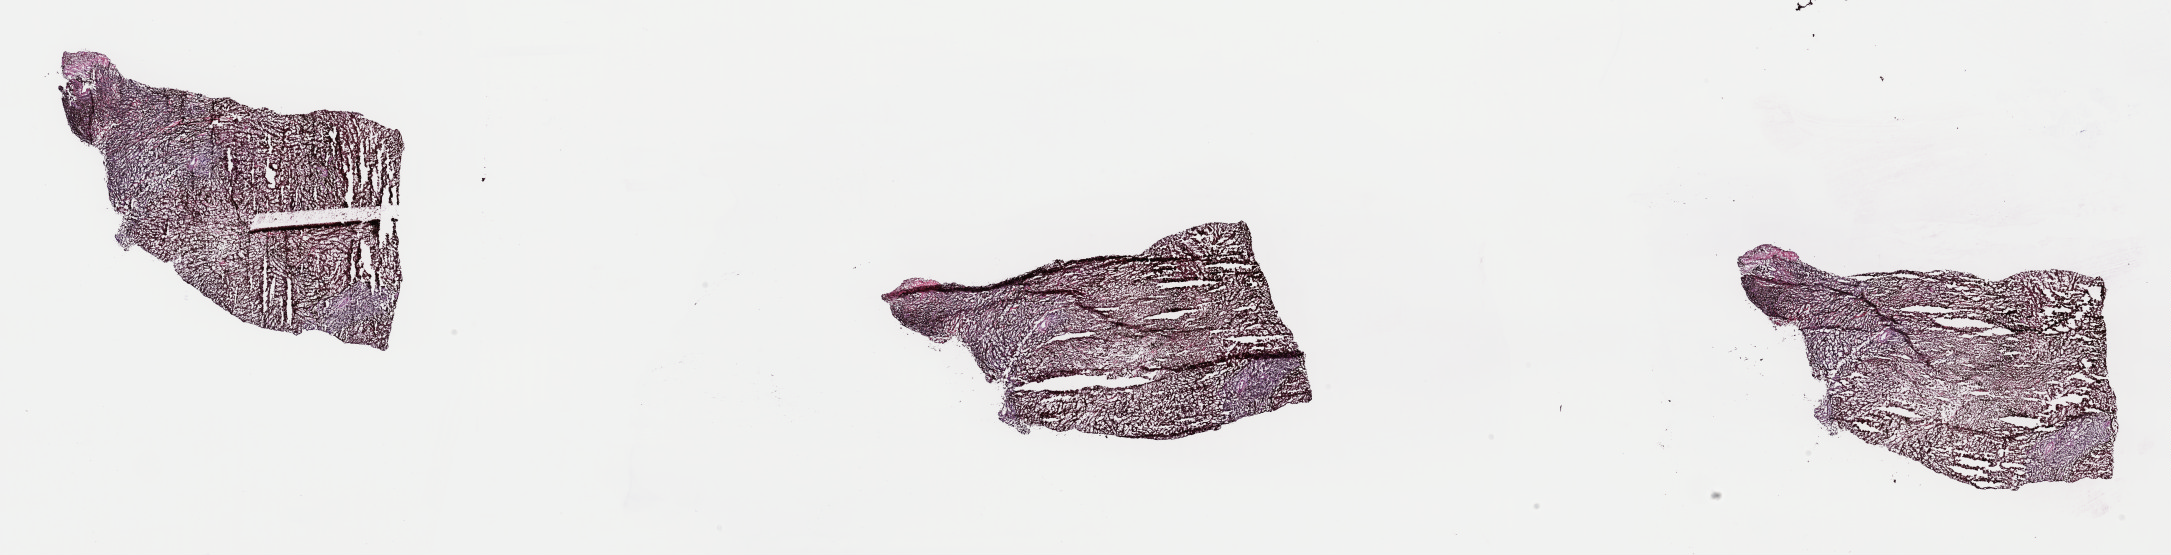
H&E-stained whole-slide image — shown as a low-resolution overview of the whole scanned area (about 34.3 x 8.8 mm, acquisition: 40x scan). Frozen section from the top of the tissue portion. Metastatic tumour sample. Male patient; age at initial diagnosis 54 years. Pathologist review of this section (percent, as recorded): tumour cells 100%, tumour nuclei 95%, normal cells 0%, stromal cells 0%, necrosis 0%. Inflammatory infiltration, as recorded: lymphocyte infiltration 0%, monocyte infiltration 0%, neutrophil infiltration 0%.
• this section: metastatic tumour tissue
• patient diagnosis: Malignant melanoma, NOS